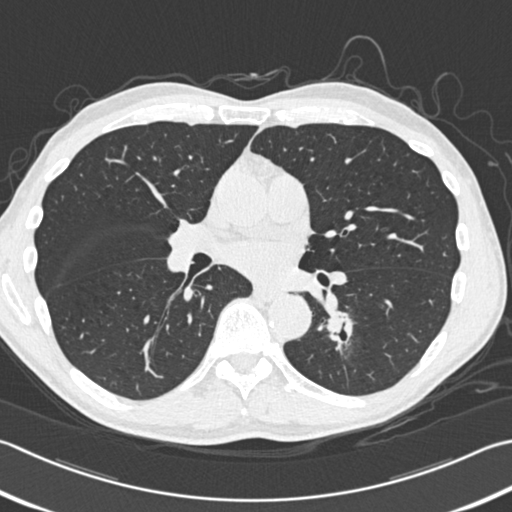
Low-dose screening chest CT, one axial slice; position 184 of 354 along the scan axis; reconstruction kernel B30f; lung window (W 1500 / L -600 HU); 1 mm slice thickness; 512 × 512 image matrix.
Outlined on this slice (expert manual segmentation):
- lesion 1 (tumor, lower lobe of left lung): bounding box (x1, y1, x2, y2) in pixels: (327, 311, 350, 337)